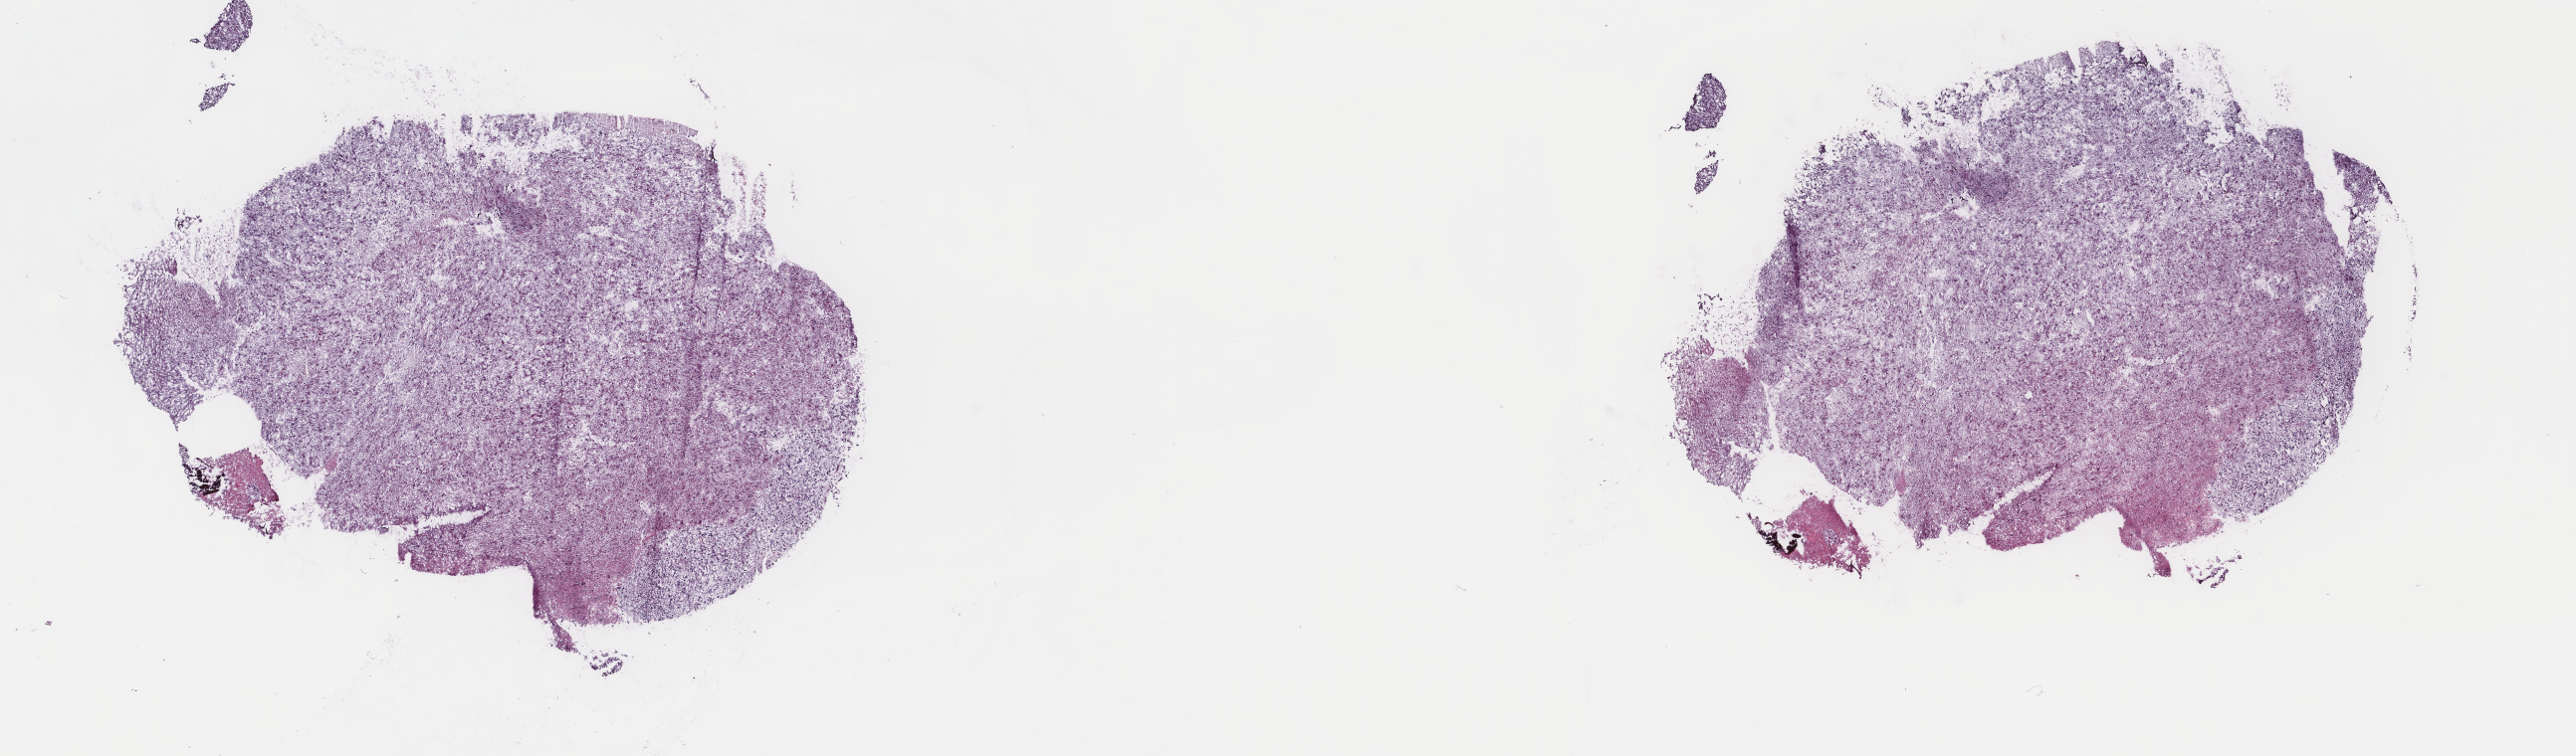
H&E whole-slide image — low-resolution overview of the scanned area, about 20.5 x 6.0 mm (acquisition: 40x scan), frozen section from the top of the tissue portion, brain, primary tumour sample. Male patient; age at initial diagnosis 70 years. Histologic grade: G3 (poorly differentiated). Pathologist review of this section (percent, as recorded): tumour cells 60%, tumour nuclei 80%, normal cells 10%, stromal cells 30%, necrosis 0%. Infiltration values recorded for this section: lymphocyte infiltration 0%, monocyte infiltration 0%, neutrophil infiltration 0%.
Diagnosis: Oligodendroglioma, anaplastic.